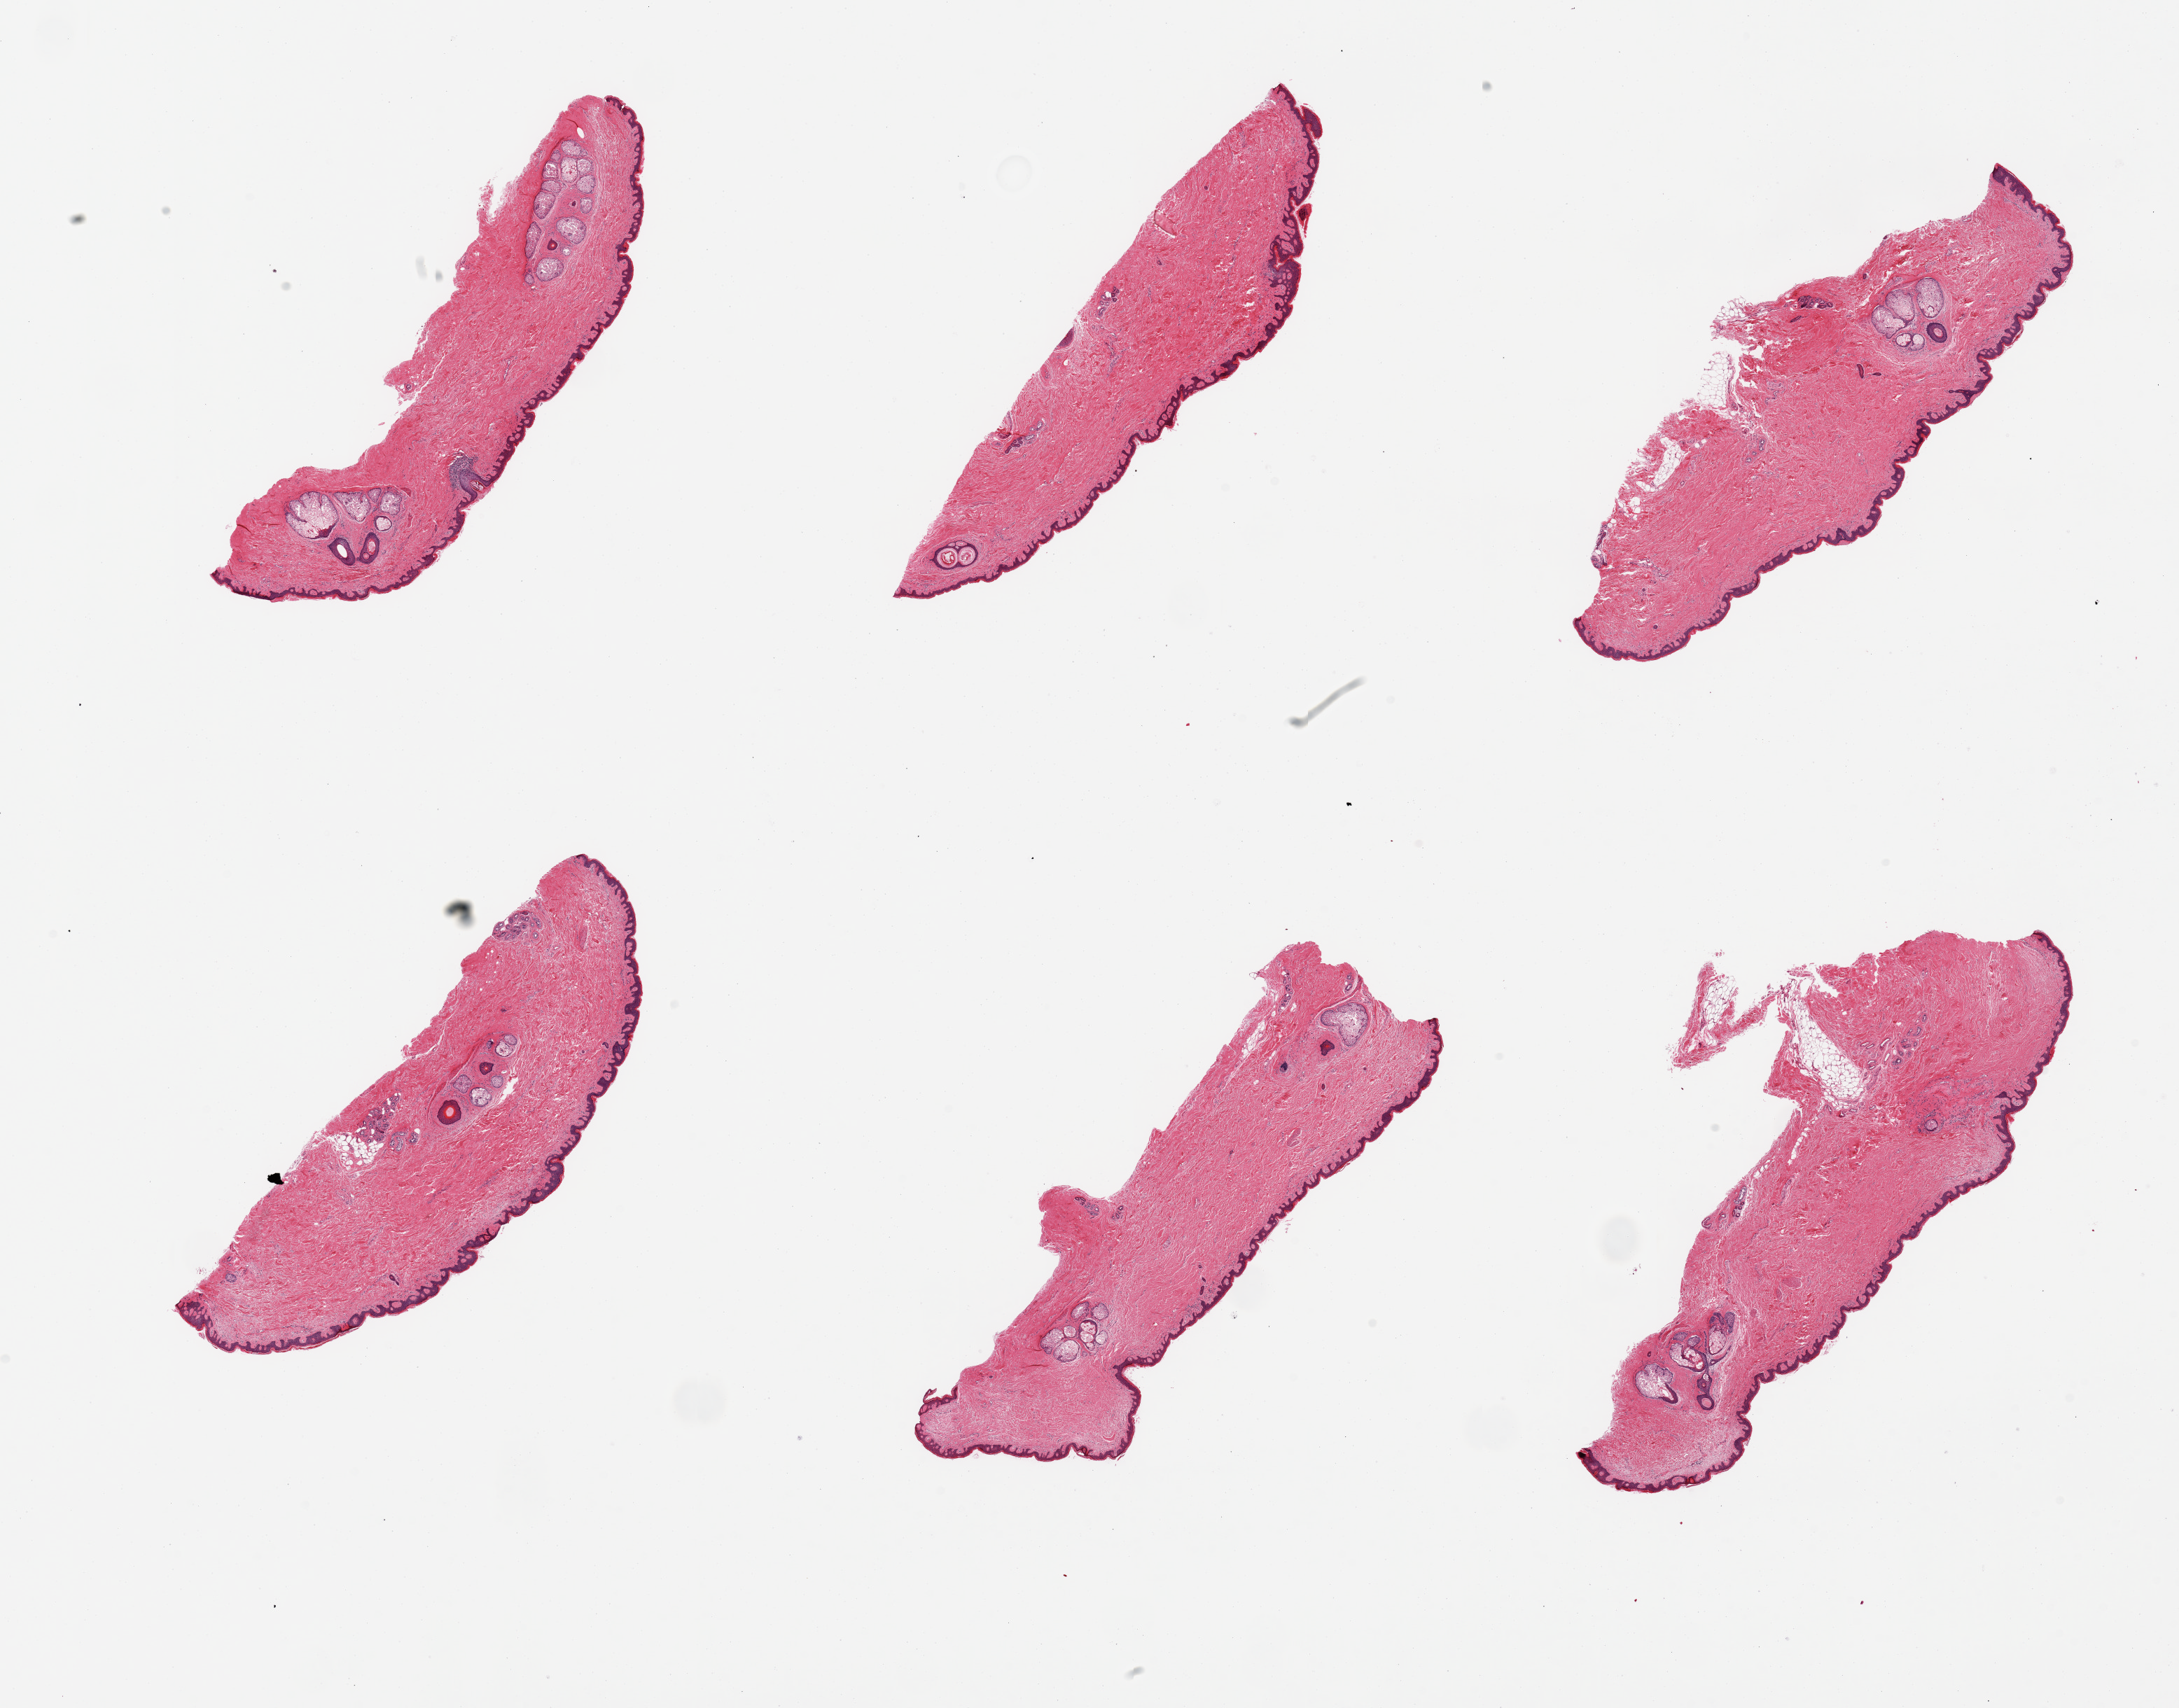
Digitized haematoxylin and eosin-stained section — a low-resolution overview of the entire scanned area, about 24.6 x 19.3 mm (from a 20x scan), PAXgene-fixed paraffin-embedded (PFPE) section, target tissue: skin of suprapubic region, donor tissue sample. Donor: male.
Pathologist's review note for this sample: 6 pieces, minimal dermal fat; squamous epithelium is ~50-60 microns.